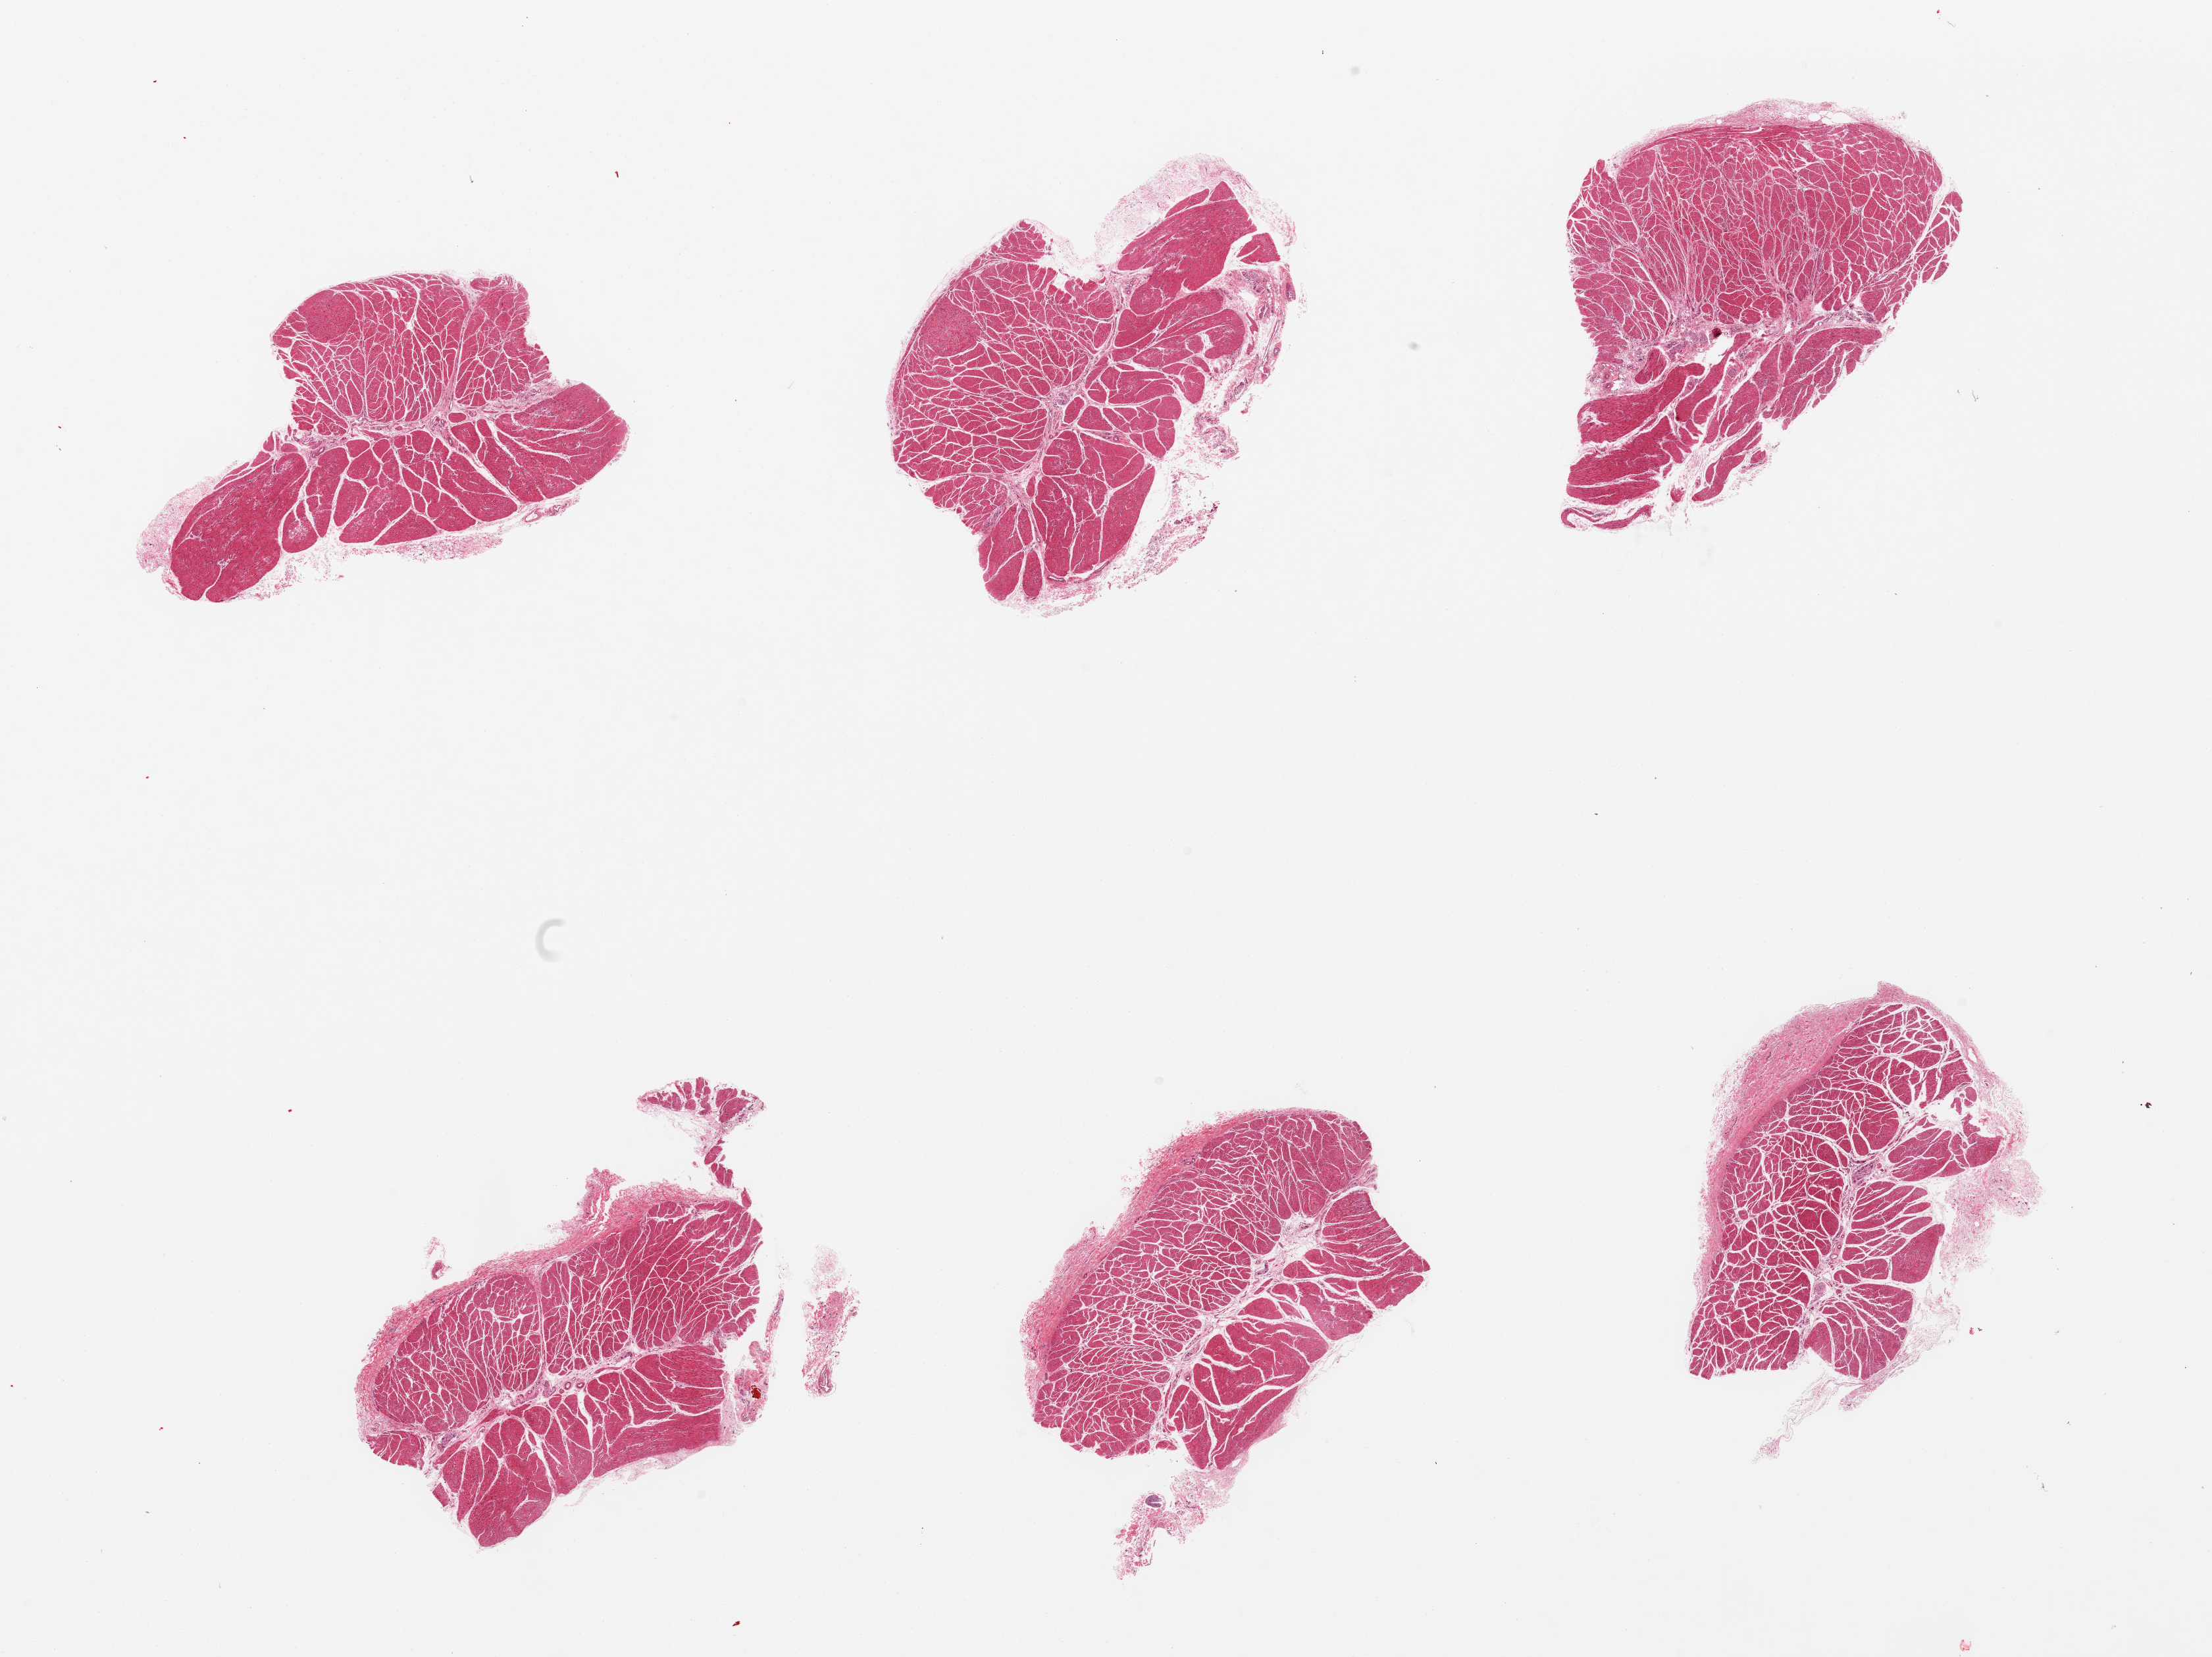
Whole-slide image, hematoxylin and eosin (H&E) stain, brightfield, a low-resolution overview of the entire scanned area, about 26.6 x 19.9 mm, PAXgene-fixed paraffin-embedded (PFPE) section, section of esophageal muscle (target tissue), tissue donor sample.
- review note (as recorded): 6 pieces, well trimmed, detached fragment of squamous mucosa